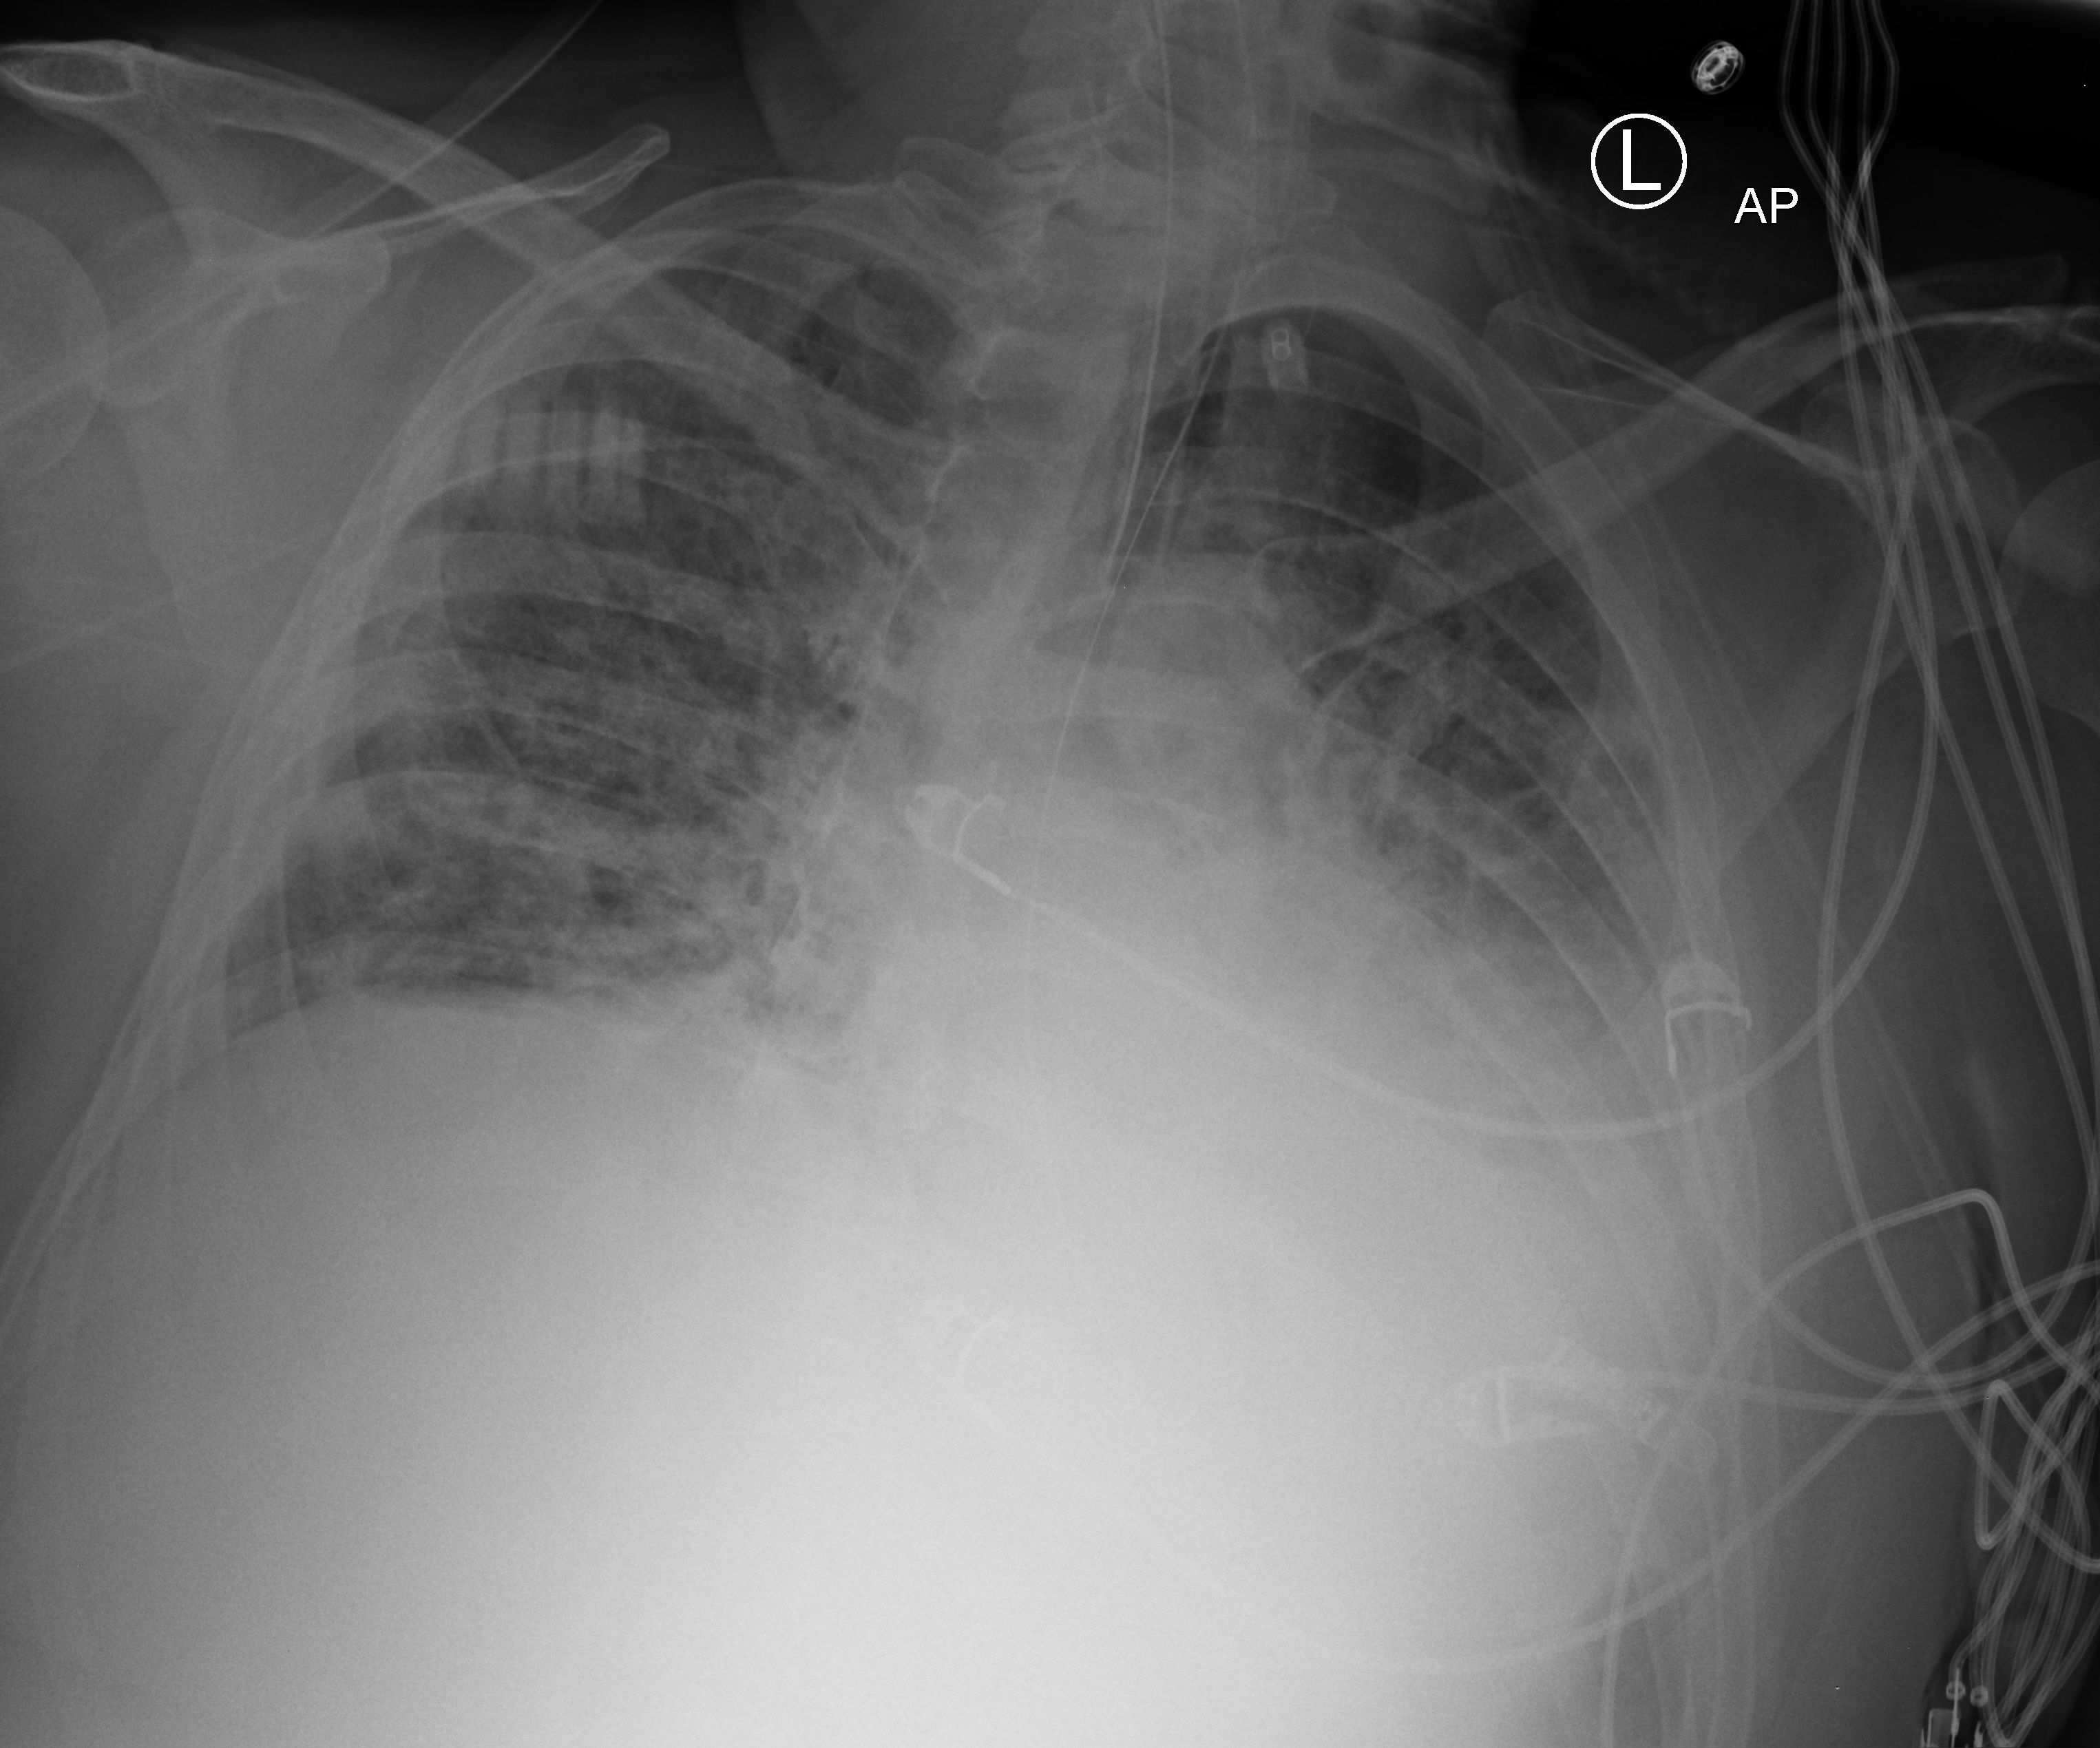
Bedside chest radiograph (computed radiography), anteroposterior (AP) projection. Male patient hospitalised with COVID-19, age 18–59 years.
Admission-level facts for this patient (not findings on this image; timing relative to this image not recorded): admitted to intensive care during this hospital stay: yes.